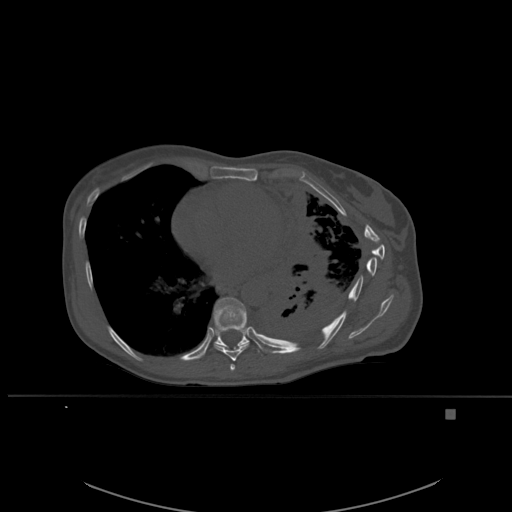
CT including the spine, one axial slice; slice 344 of 537 in the series (ordered by position); bone window (W 1800 / L 400 HU); 1.5 mm slice thickness; 512 × 512 image matrix, field of view 440 × 440 mm. Female patient, age 45 years. Case-level facts recorded for this patient, not image findings: primary cancer: lung.
Annotated regions visible in this slice (semi-automatically segmented with operator editing):
- T7 vertebra: bounding box (x1, y1, x2, y2) in pixels: (230, 364, 235, 371)
- T8 vertebra: (214, 343, 249, 361)
- T9 vertebra: (213, 297, 250, 349)